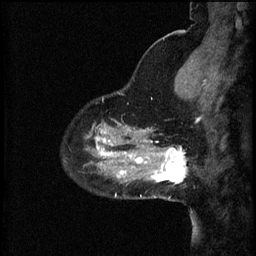
Breast MRI (dynamic contrast-enhanced), one sagittal slice; position 14 of 60 along the scan axis; 3 images stored at this slice position (order not interpretable as contrast timing); 1.5 T; TE 4.2 ms, TR 8.2 ms; 256 × 256 image matrix, field of view 200 × 200 mm. Female patient, age 37 years.
Outlined on this slice (semi-automatically segmented with operator editing):
- analysis volume of interest (the breast-tissue region the enhancement analysis was run in; not a lesion): box from (x=148, y=140) to (x=189, y=183) px
- tumour enhancement mask (voxels above the 70 % enhancement threshold inside the analysis volume of interest): (x=148, y=140)–(x=187, y=183)